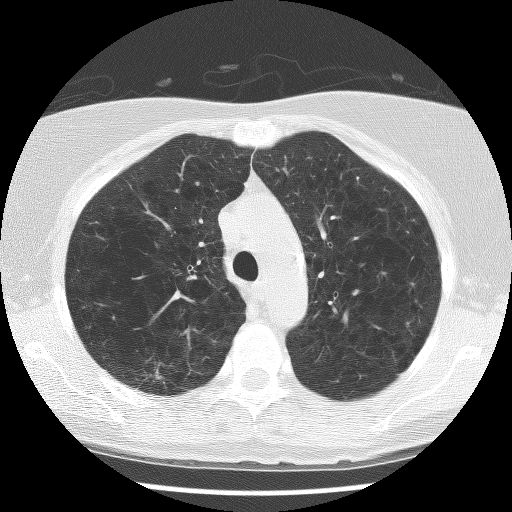
Axial slice from a low-dose chest CT screening exam. First (baseline) screen. Lung window (W 1500 / L -600 HU). 2.5 mm slice thickness. Lung (sharp) reconstruction kernel (BONE). Slice 36 of 129 in the series. 512 × 512 image matrix, field of view 310 × 310 mm. Female, age 63 years at enrolment. Former smoker at enrolment.
Lesion marked by an expert reader, box from (x=126, y=355) to (x=186, y=406) px. Screening reader's record for this exam (one nodule recorded; not confirmed to be the boxed lesion): non-calcified nodule or mass ≥4 mm, right upper lobe, 9 × 6 mm, spiculated (stellate) margins, mixed attenuation. Official screen result: positive, change unspecified: nodule(s) >= 4 mm or enlarging nodule(s), mass(es), or other non-specific abnormalities suspicious for lung cancer. Lung cancer was diagnosed 350 days after this screen: bronchiolo-alveolar carcinoma, non-mucinous, right upper lobe, well differentiated (G1), stage IA (AJCC 6th edition), 12 mm at pathology.